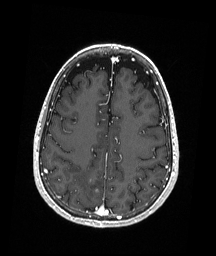
Brain MRI from a brain-tumour surgery series, one axial slice; slice 72 of 192 in the series (ordered by position); T1-weighted post-contrast; 1 mm slice thickness; 216 × 256 image matrix. Case-level facts recorded for this patient, not image findings: histopathology: Astrocytoma; WHO grade: 3; IDH mutation: yes; tumour location: Right Parietal.
Structures marked on this image (outlined manually by an expert reader):
- tumour: box from (x=89, y=179) to (x=99, y=192) px